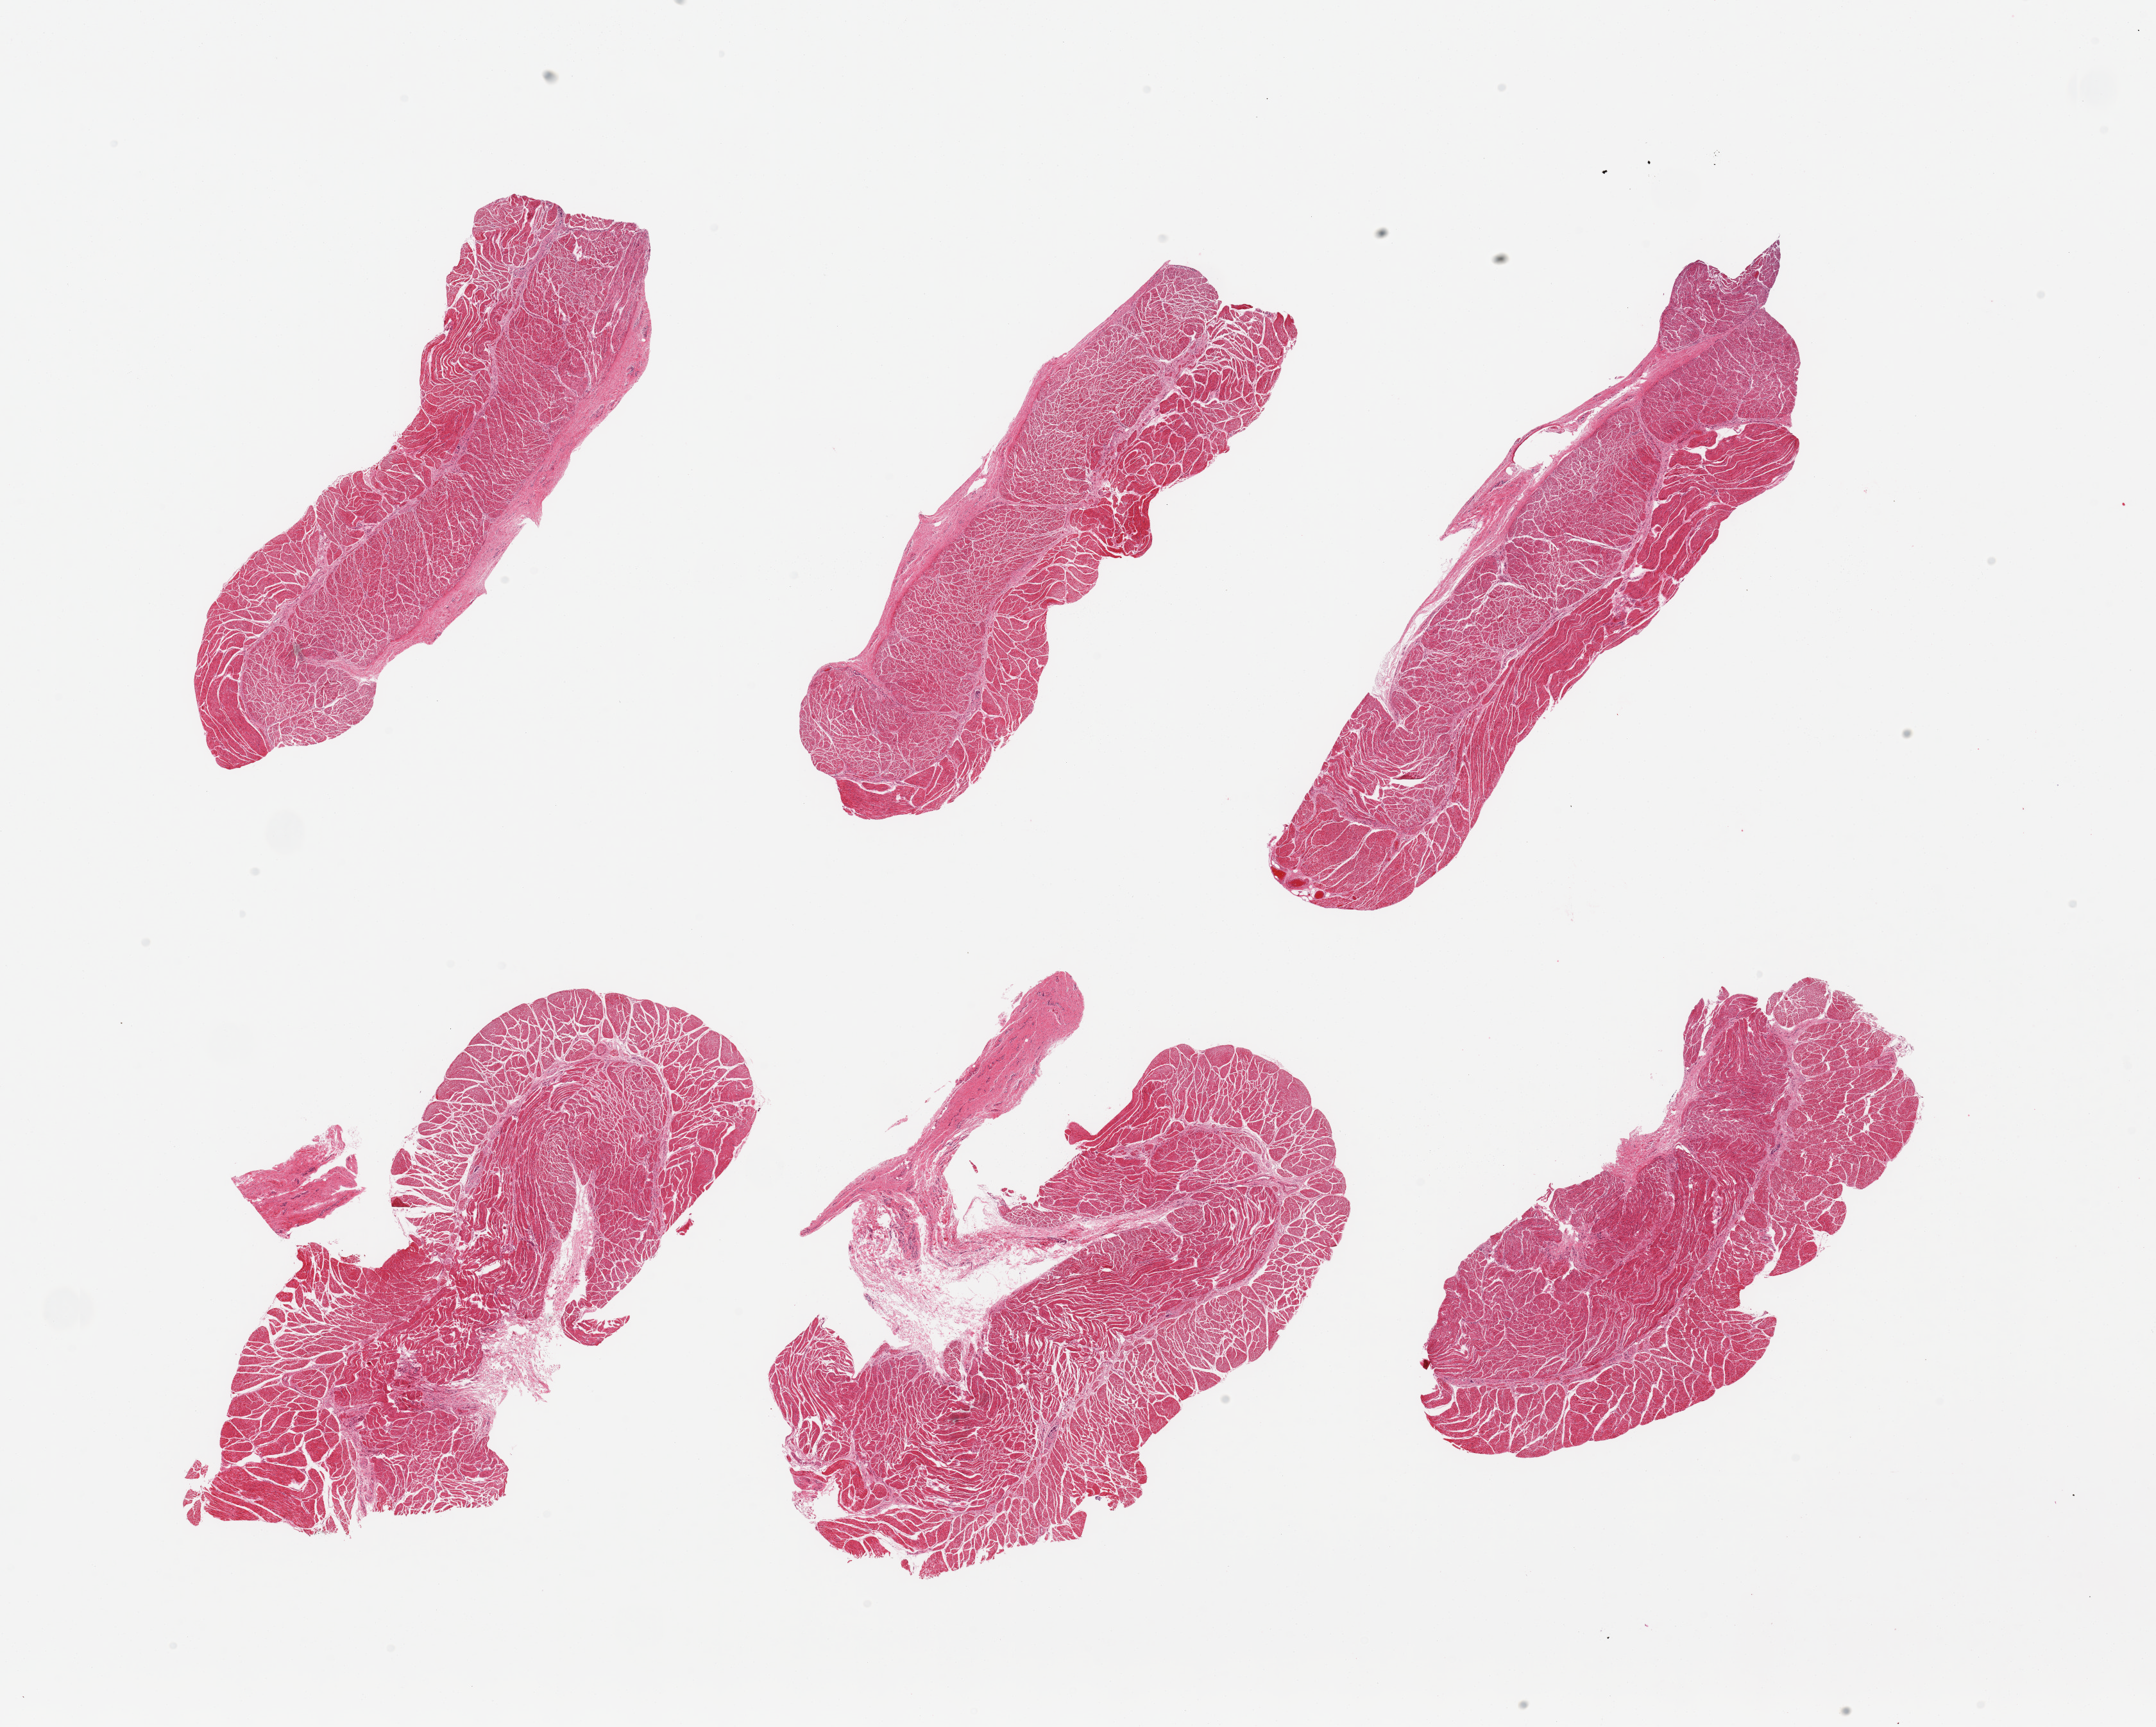
Digitized H&E-stained section — shown as a low-resolution overview of the whole scanned area (about 26.6 x 21.3 mm, slide scanned at 20x). PAXgene-fixed, paraffin-embedded tissue. Target tissue: esophageal muscle. Tissue donor sample. Donor sex: male.
• pathologist's review note for this sample: 6 pieces, confirmed target muscularis